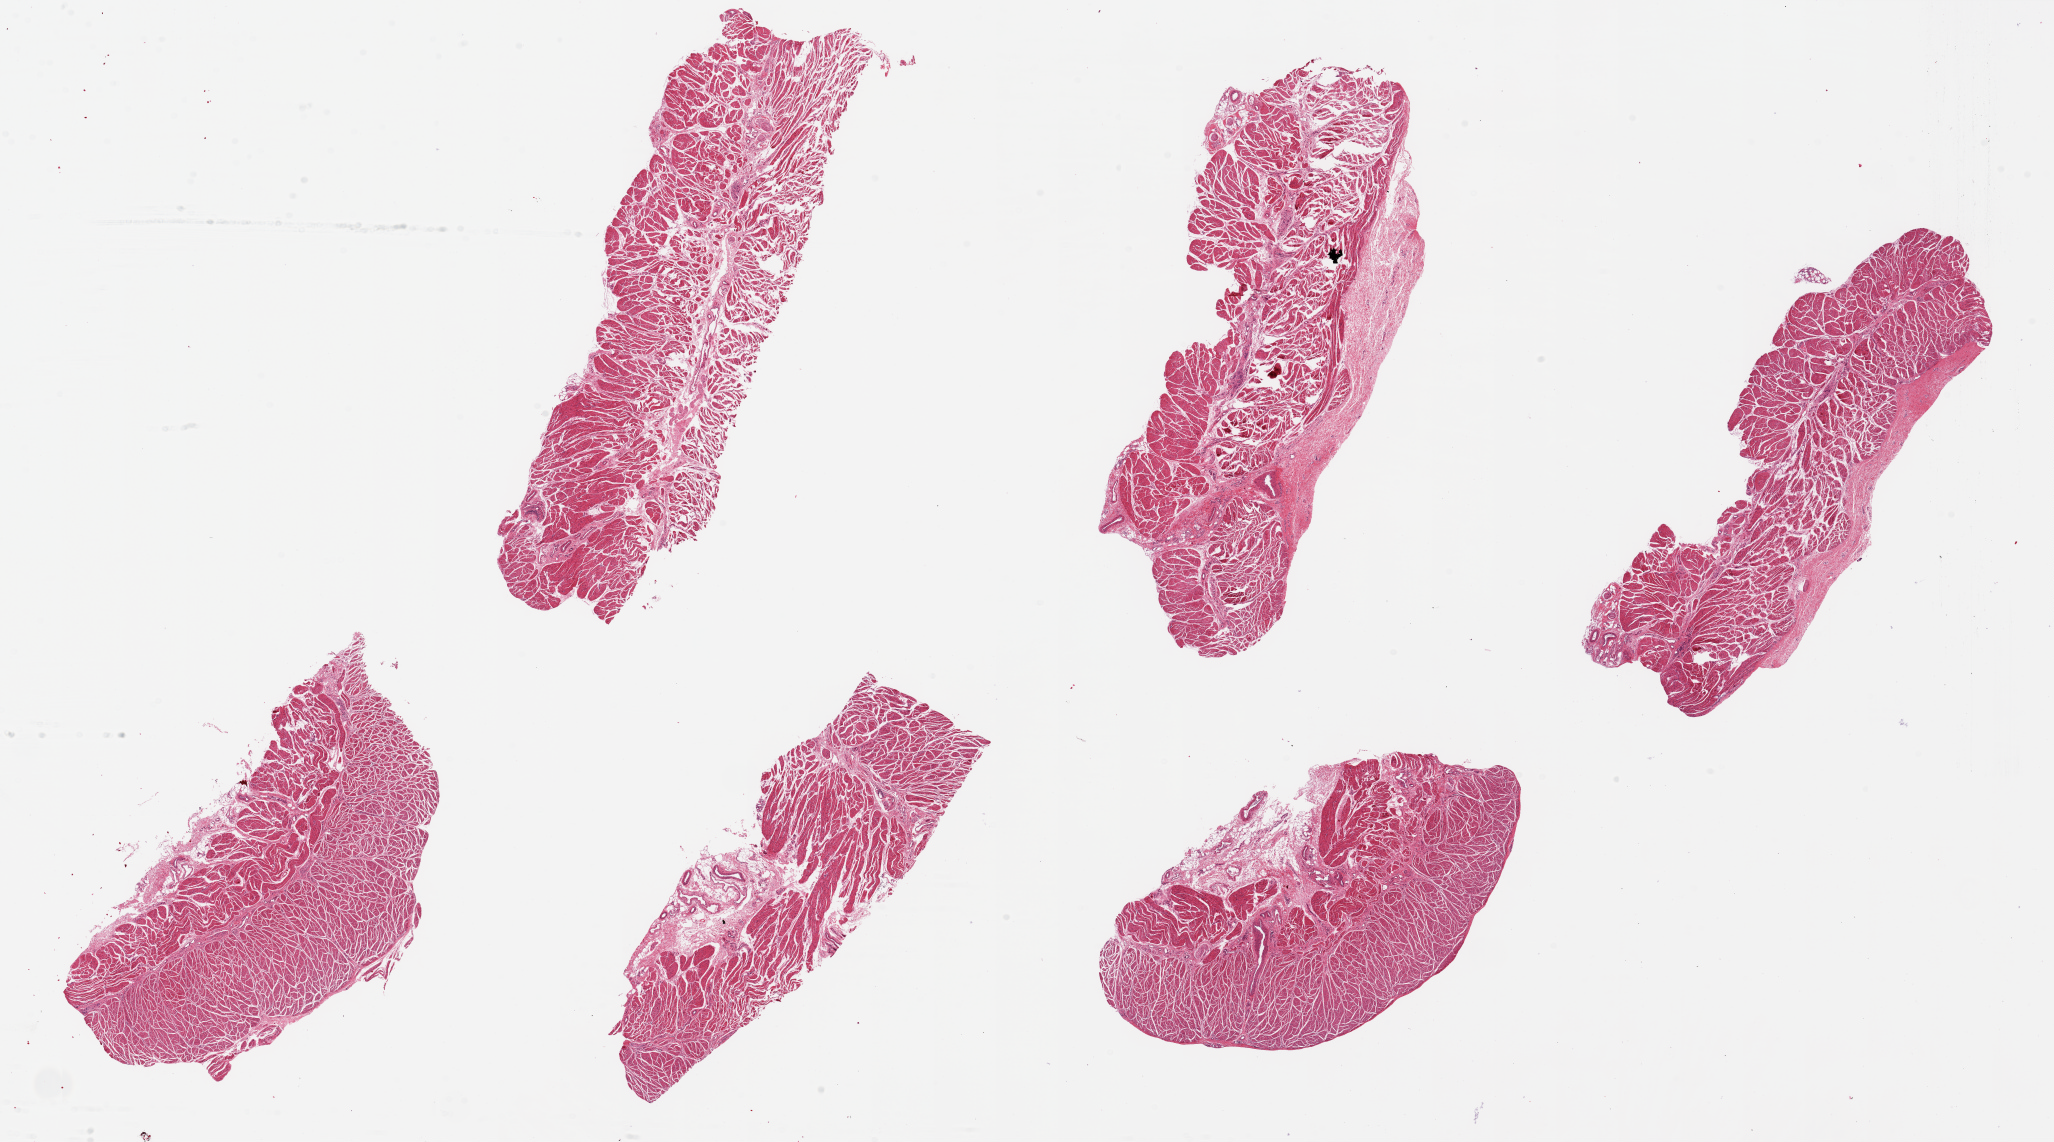
Digitized haematoxylin and eosin-stained section, brightfield — a low-resolution overview of the entire scanned area, about 32.5 x 18.1 mm (acquisition: 20x scan), PAXgene-fixed, paraffin-embedded tissue, section of esophageal muscle (target tissue), tissue donor sample.
- pathologist's review note for this sample: 6 pieces ~9x3mm, good specimens, all muscle